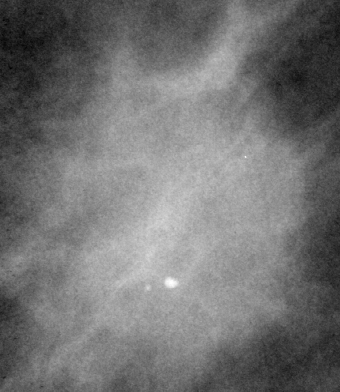
Cropped region of a digitized screen-film mammogram centred on a radiologist-marked abnormality, right breast, MLO view.
Marked abnormality: mass, shape irregular / architectural distortion, margins spiculated; BI-RADS assessment category 4; subtlety rating 5 on a 1 (subtle) to 5 (obvious) scale; pathology (as recorded): malignant.